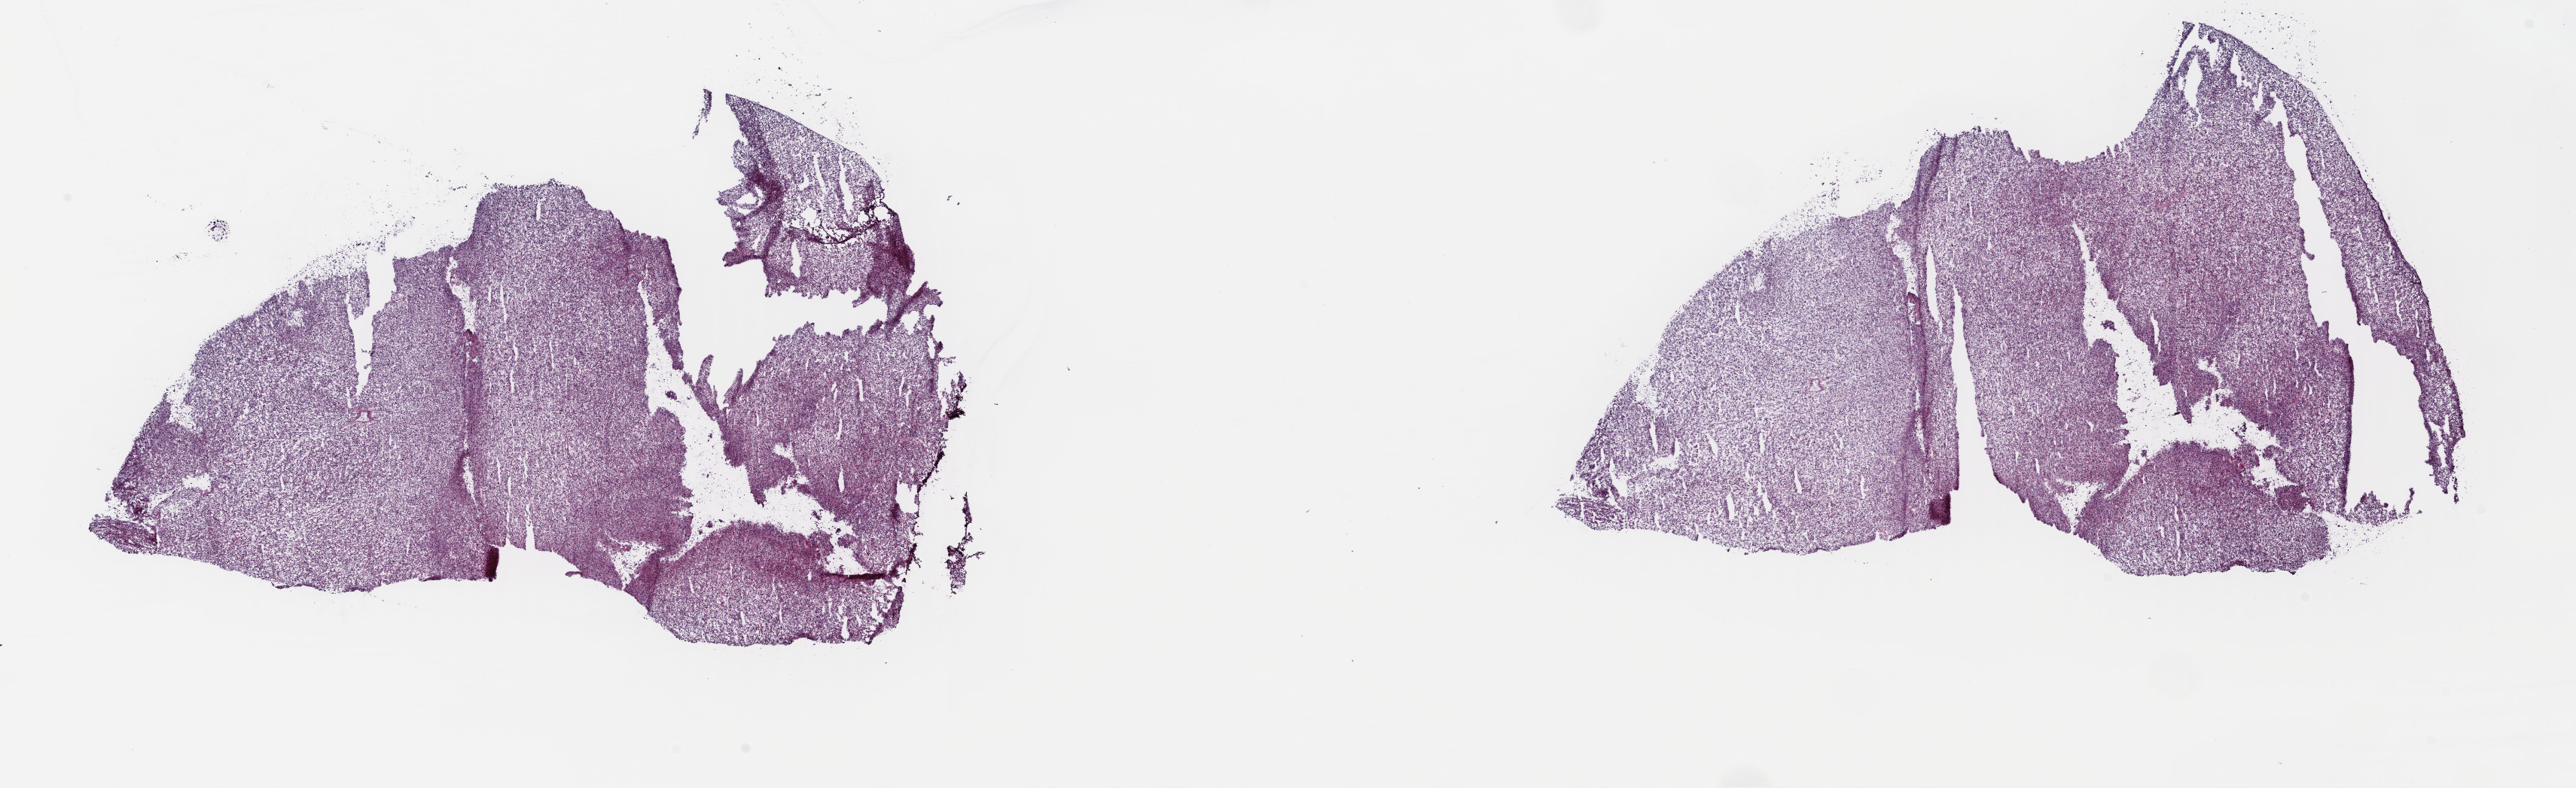
Digitized H&E-stained tissue section (whole slide), whole scanned area (about 26.9 x 8.2 mm, slide scanned at 40x) shown as a low-resolution overview. Frozen section. Sample: primary tumour, uterus. Female, age 87 years at initial diagnosis. Pathologist review of this section (percent, as recorded): tumour cells 95%, tumour nuclei 100%.
Diagnosis: Mullerian mixed tumor (endometrium).